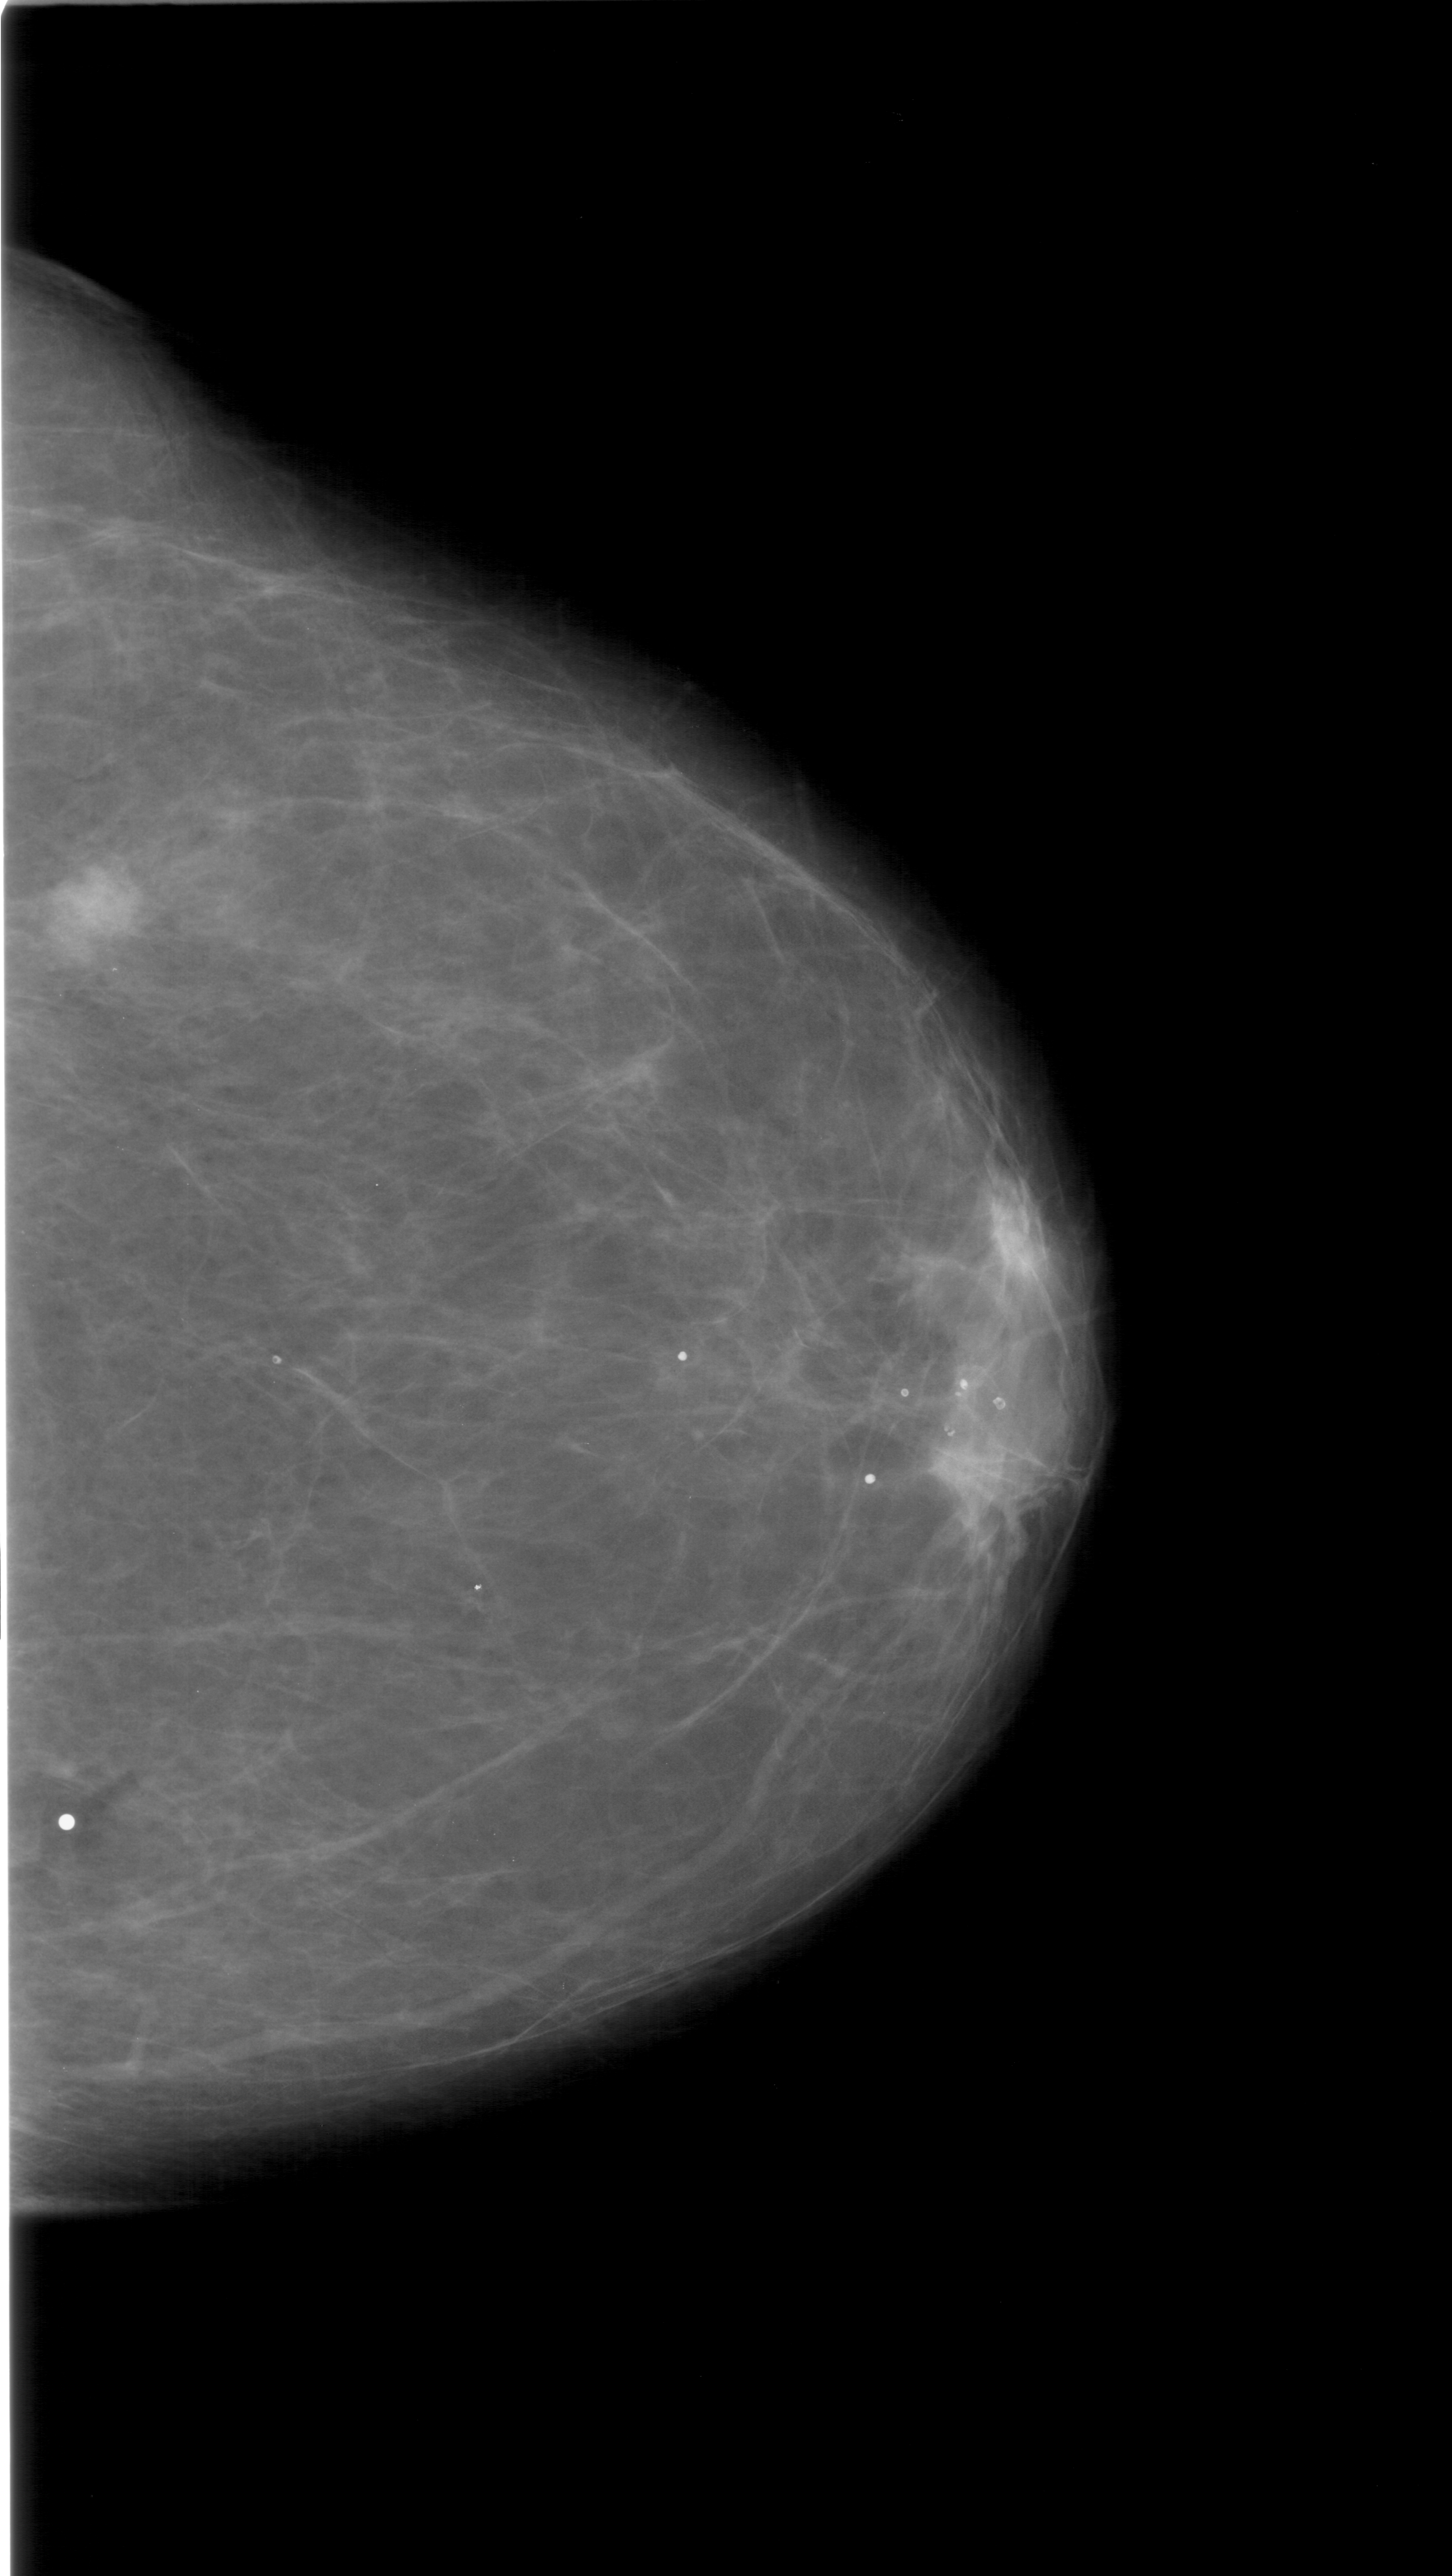
Digitized screen-film mammogram; right breast; craniocaudal (CC) view; BI-RADS breast density category 1 (scale 1–4).
Abnormality record for this image: mass, shape irregular, margins ill defined; BI-RADS assessment category 5; pathology result (as recorded, not read from the image): malignant.